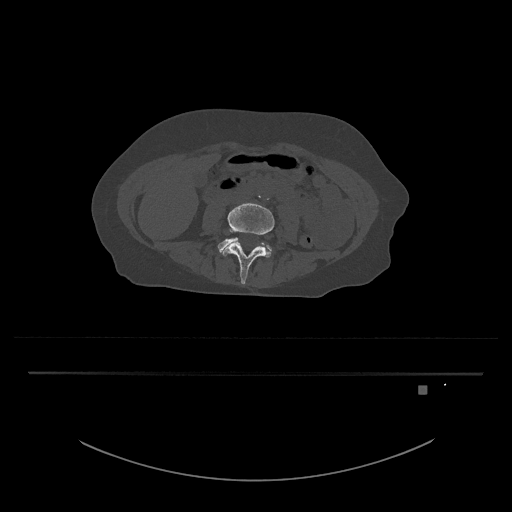
CT including the spine, one axial slice; reconstruction kernel Br40s/3; bone window (W 1800 / L 400 HU); 0.5 mm slice thickness; 512 × 512 image matrix, field of view 500 × 500 mm. Female patient, age 57 years. Case-level facts recorded for this patient, not image findings: primary cancer: cervical.
Outlined on this slice (semi-automatically segmented with operator editing):
- L4 vertebra: bounding box <220,203,275,285> (left, top, right, bottom; pixels)